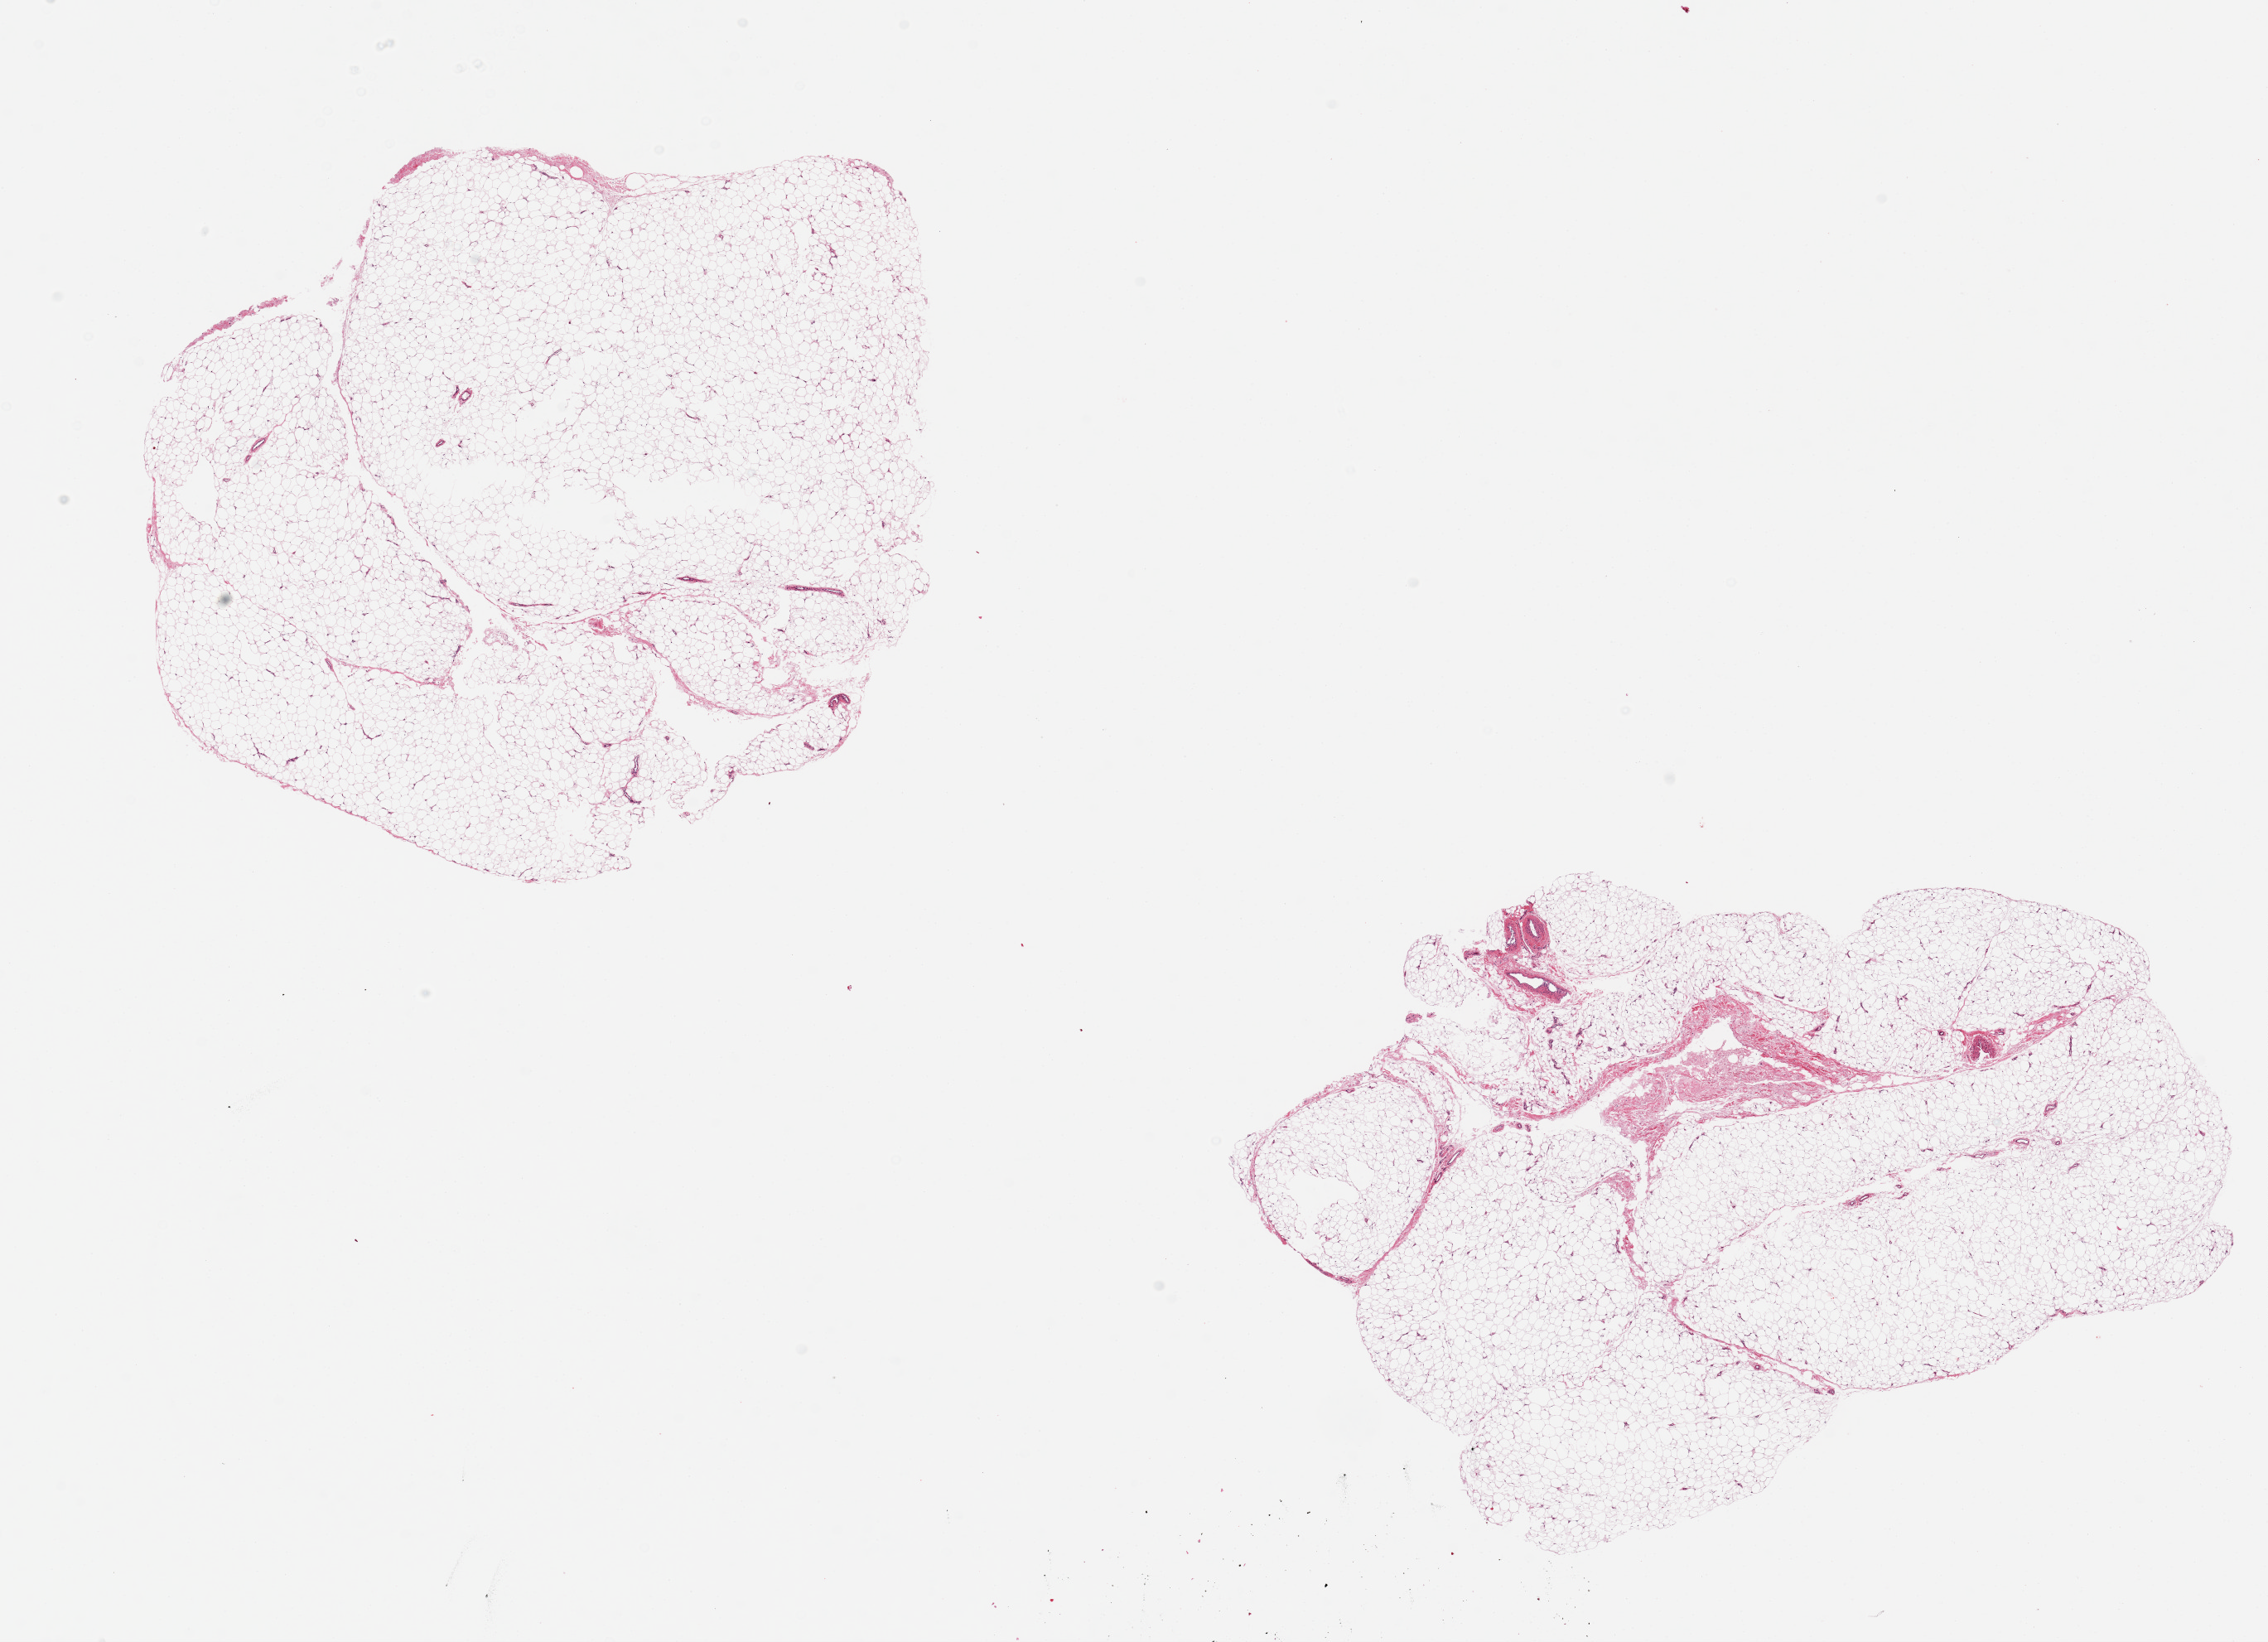
Digitized hematoxylin and eosin (H&E)-stained section, shown as a low-resolution overview of the whole scanned area (about 21.7 x 15.7 mm); PAXgene-fixed paraffin-embedded (PFPE) section; target tissue: adipose tissue; tissue donor sample. Donor: female.
Reviewer comment on this tissue sample: 2 aliquots, 8x6mm.